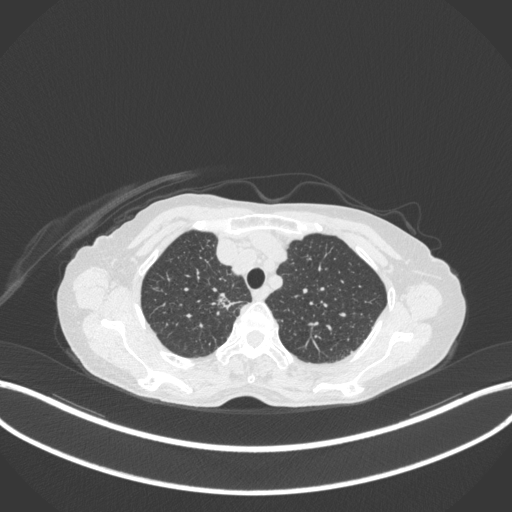
Chest CT, one axial slice; slice 302 of 363 in the series (ordered by position); reconstruction kernel B31f; 120 kVp; lung window (W 1500 / L -600 HU); 512 × 512 image matrix, field of view 400 × 400 mm. Patient: female, 75 years. From the clinical record (not read from this slice): clinical TNM (as recorded): T1c N1 M1.
Structures marked on this image (bounding box drawn by a radiologist):
- lung tumour (recorded histology: adenocarcinoma): box from (x=210, y=286) to (x=243, y=311) px